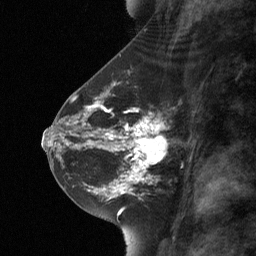
Breast MRI (dynamic contrast-enhanced), one sagittal slice; slice 31 of 64 in the series (ordered by position); dynamic contrast-enhanced study with each time point stored as its own series, time point 2 of 3 at this slice position (early post-contrast, ordered by acquisition time); 1.5 T; TE 4.8 ms, TR 27 ms; 2 mm slice thickness; 256 × 256 image matrix, field of view 180 × 180 mm. Female patient, age 42 years. Case-level facts recorded for this patient, not image findings: setting: breast cancer imaged before/during neoadjuvant chemotherapy; receptor status: triple-negative.
Annotated regions visible in this slice (semi-automatic segmentation, software-assisted and operator-edited):
- analysis volume of interest (the breast-tissue region the enhancement analysis was run in; not a lesion): box from (x=111, y=117) to (x=169, y=178) px
- tumour enhancement mask (voxels above the 90 % enhancement threshold inside the analysis volume of interest): (x=111, y=132)–(x=161, y=178)